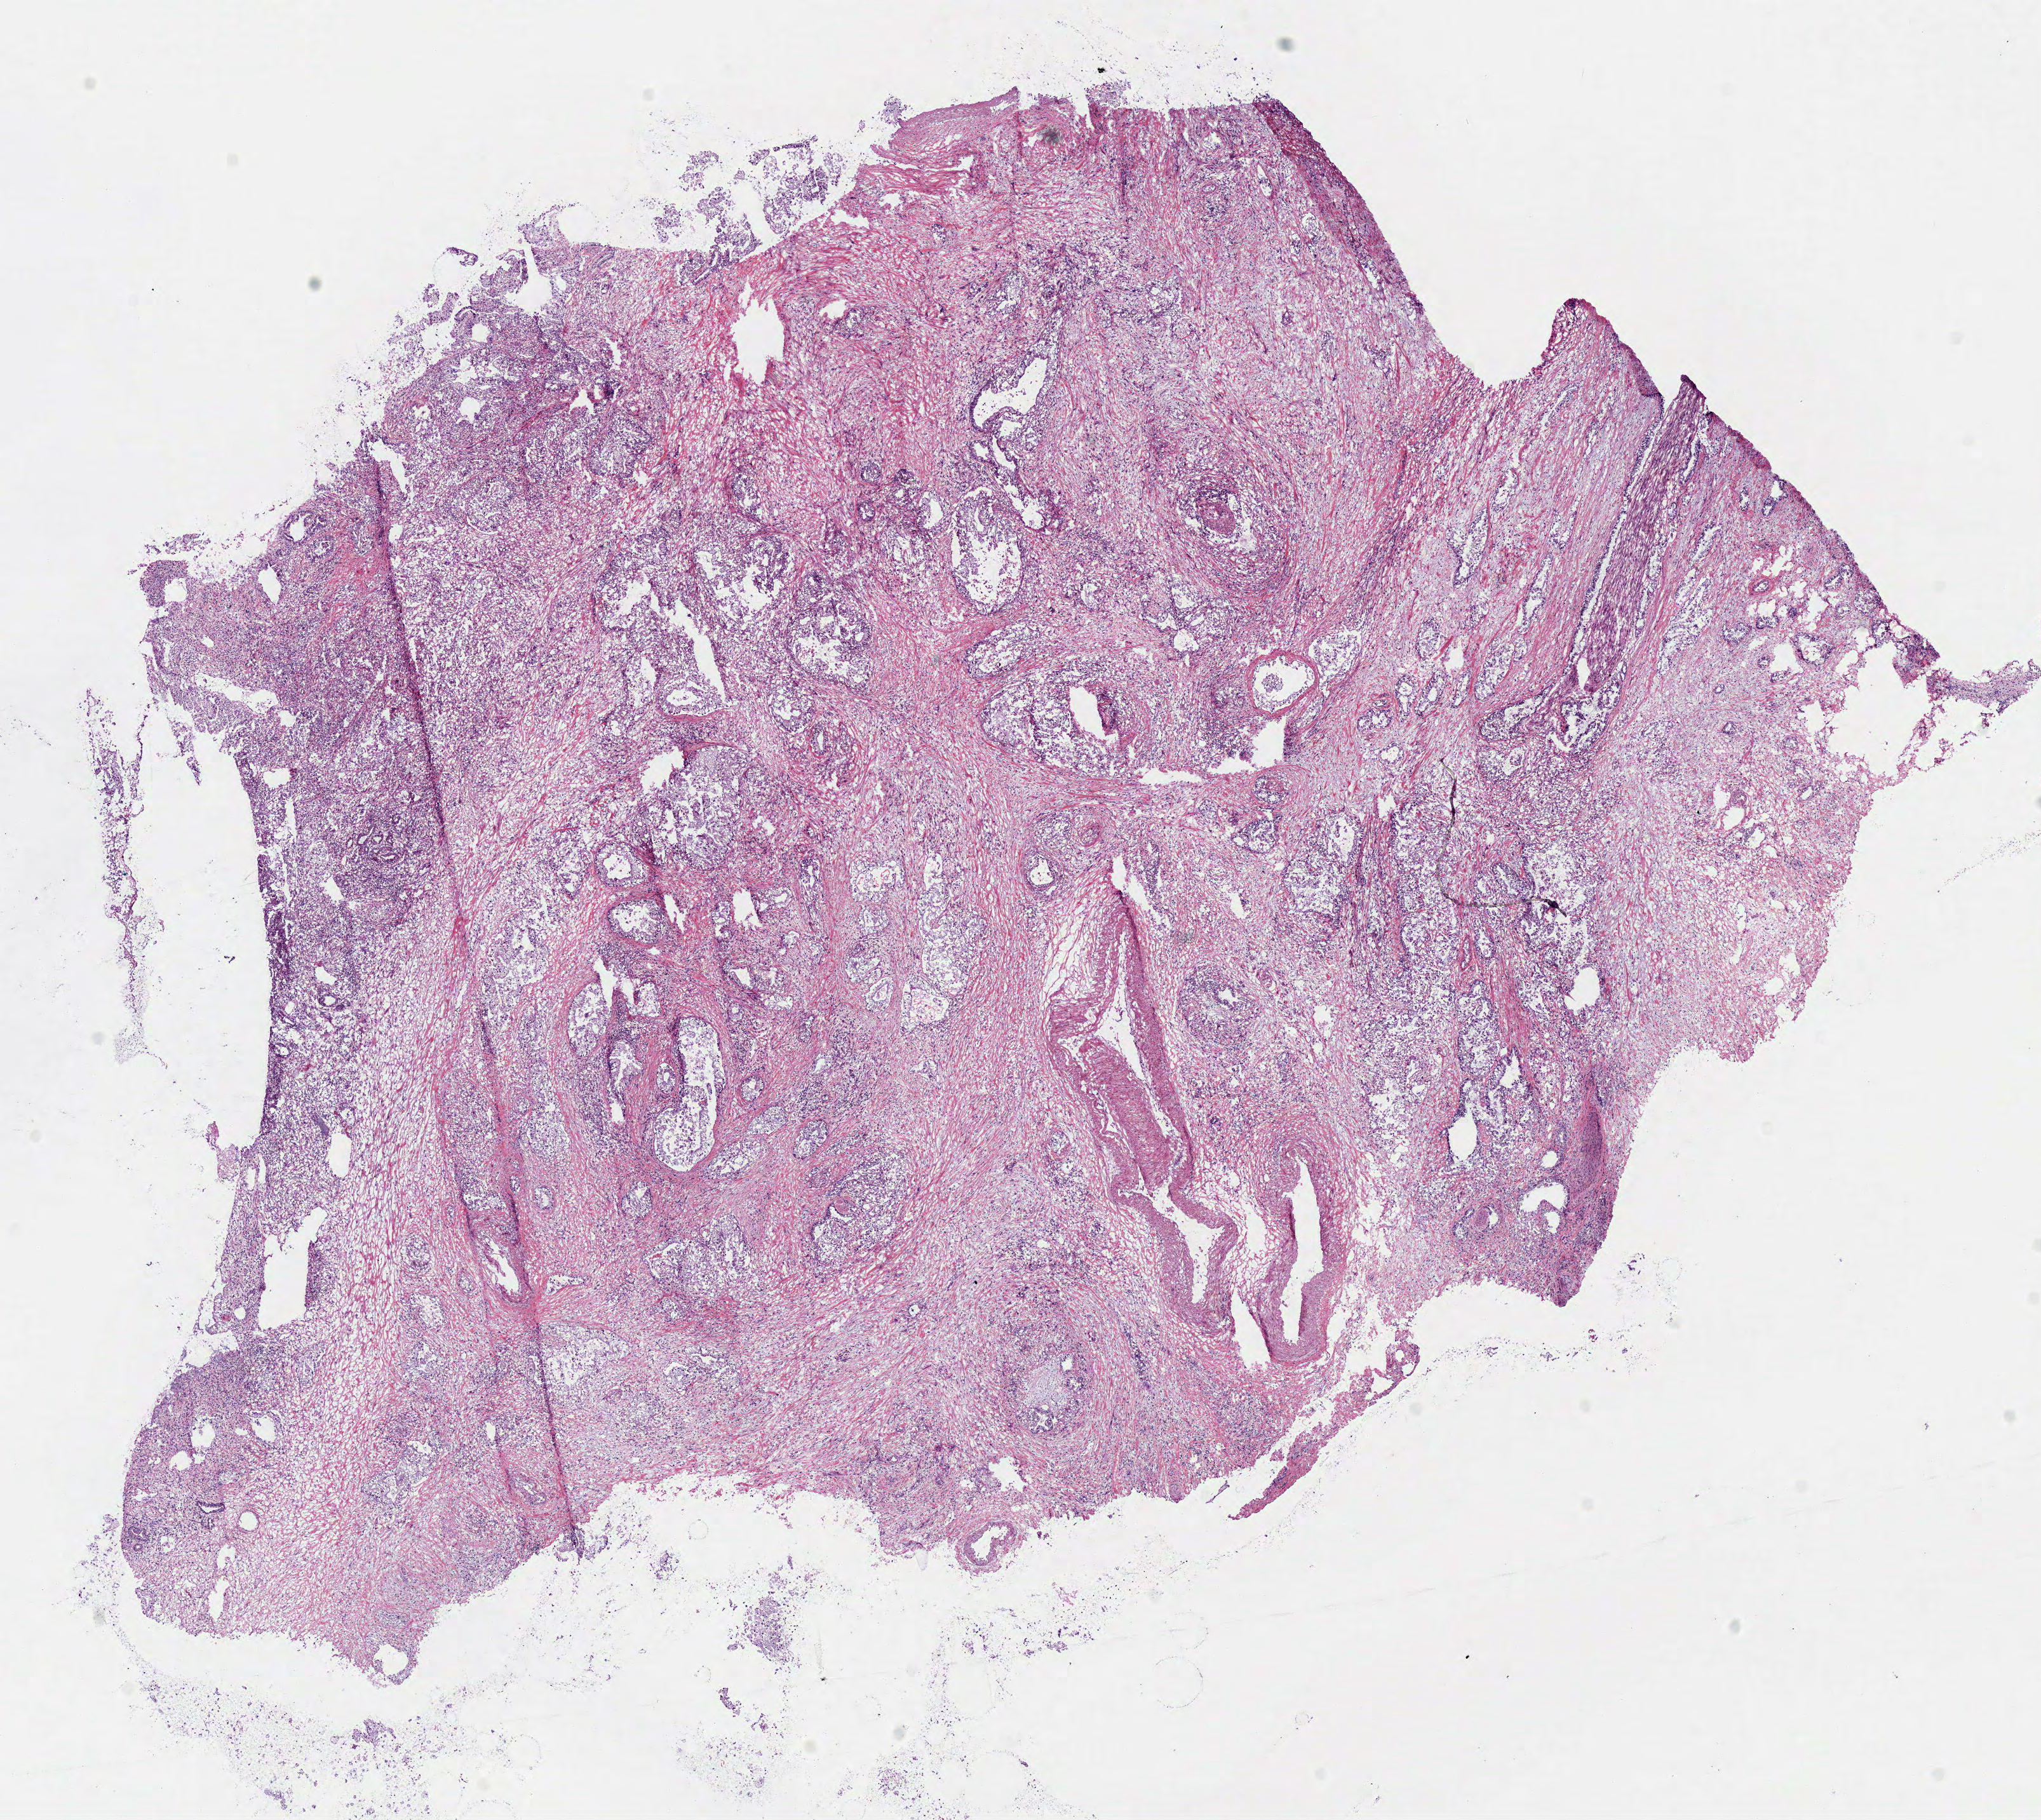
Digitized H&E-stained tissue section (whole slide) — low-resolution overview of the scanned area, about 12.7 x 11.3 mm; frozen section from the top of the tissue portion; primary tumour sample from the pancreas. Patient: female, age at initial diagnosis 85 years. Pathologist review of this section (percent, as recorded): tumour cells 70%, tumour nuclei 75%.
Pathologic diagnosis: Infiltrating duct carcinoma, NOS (head of pancreas).